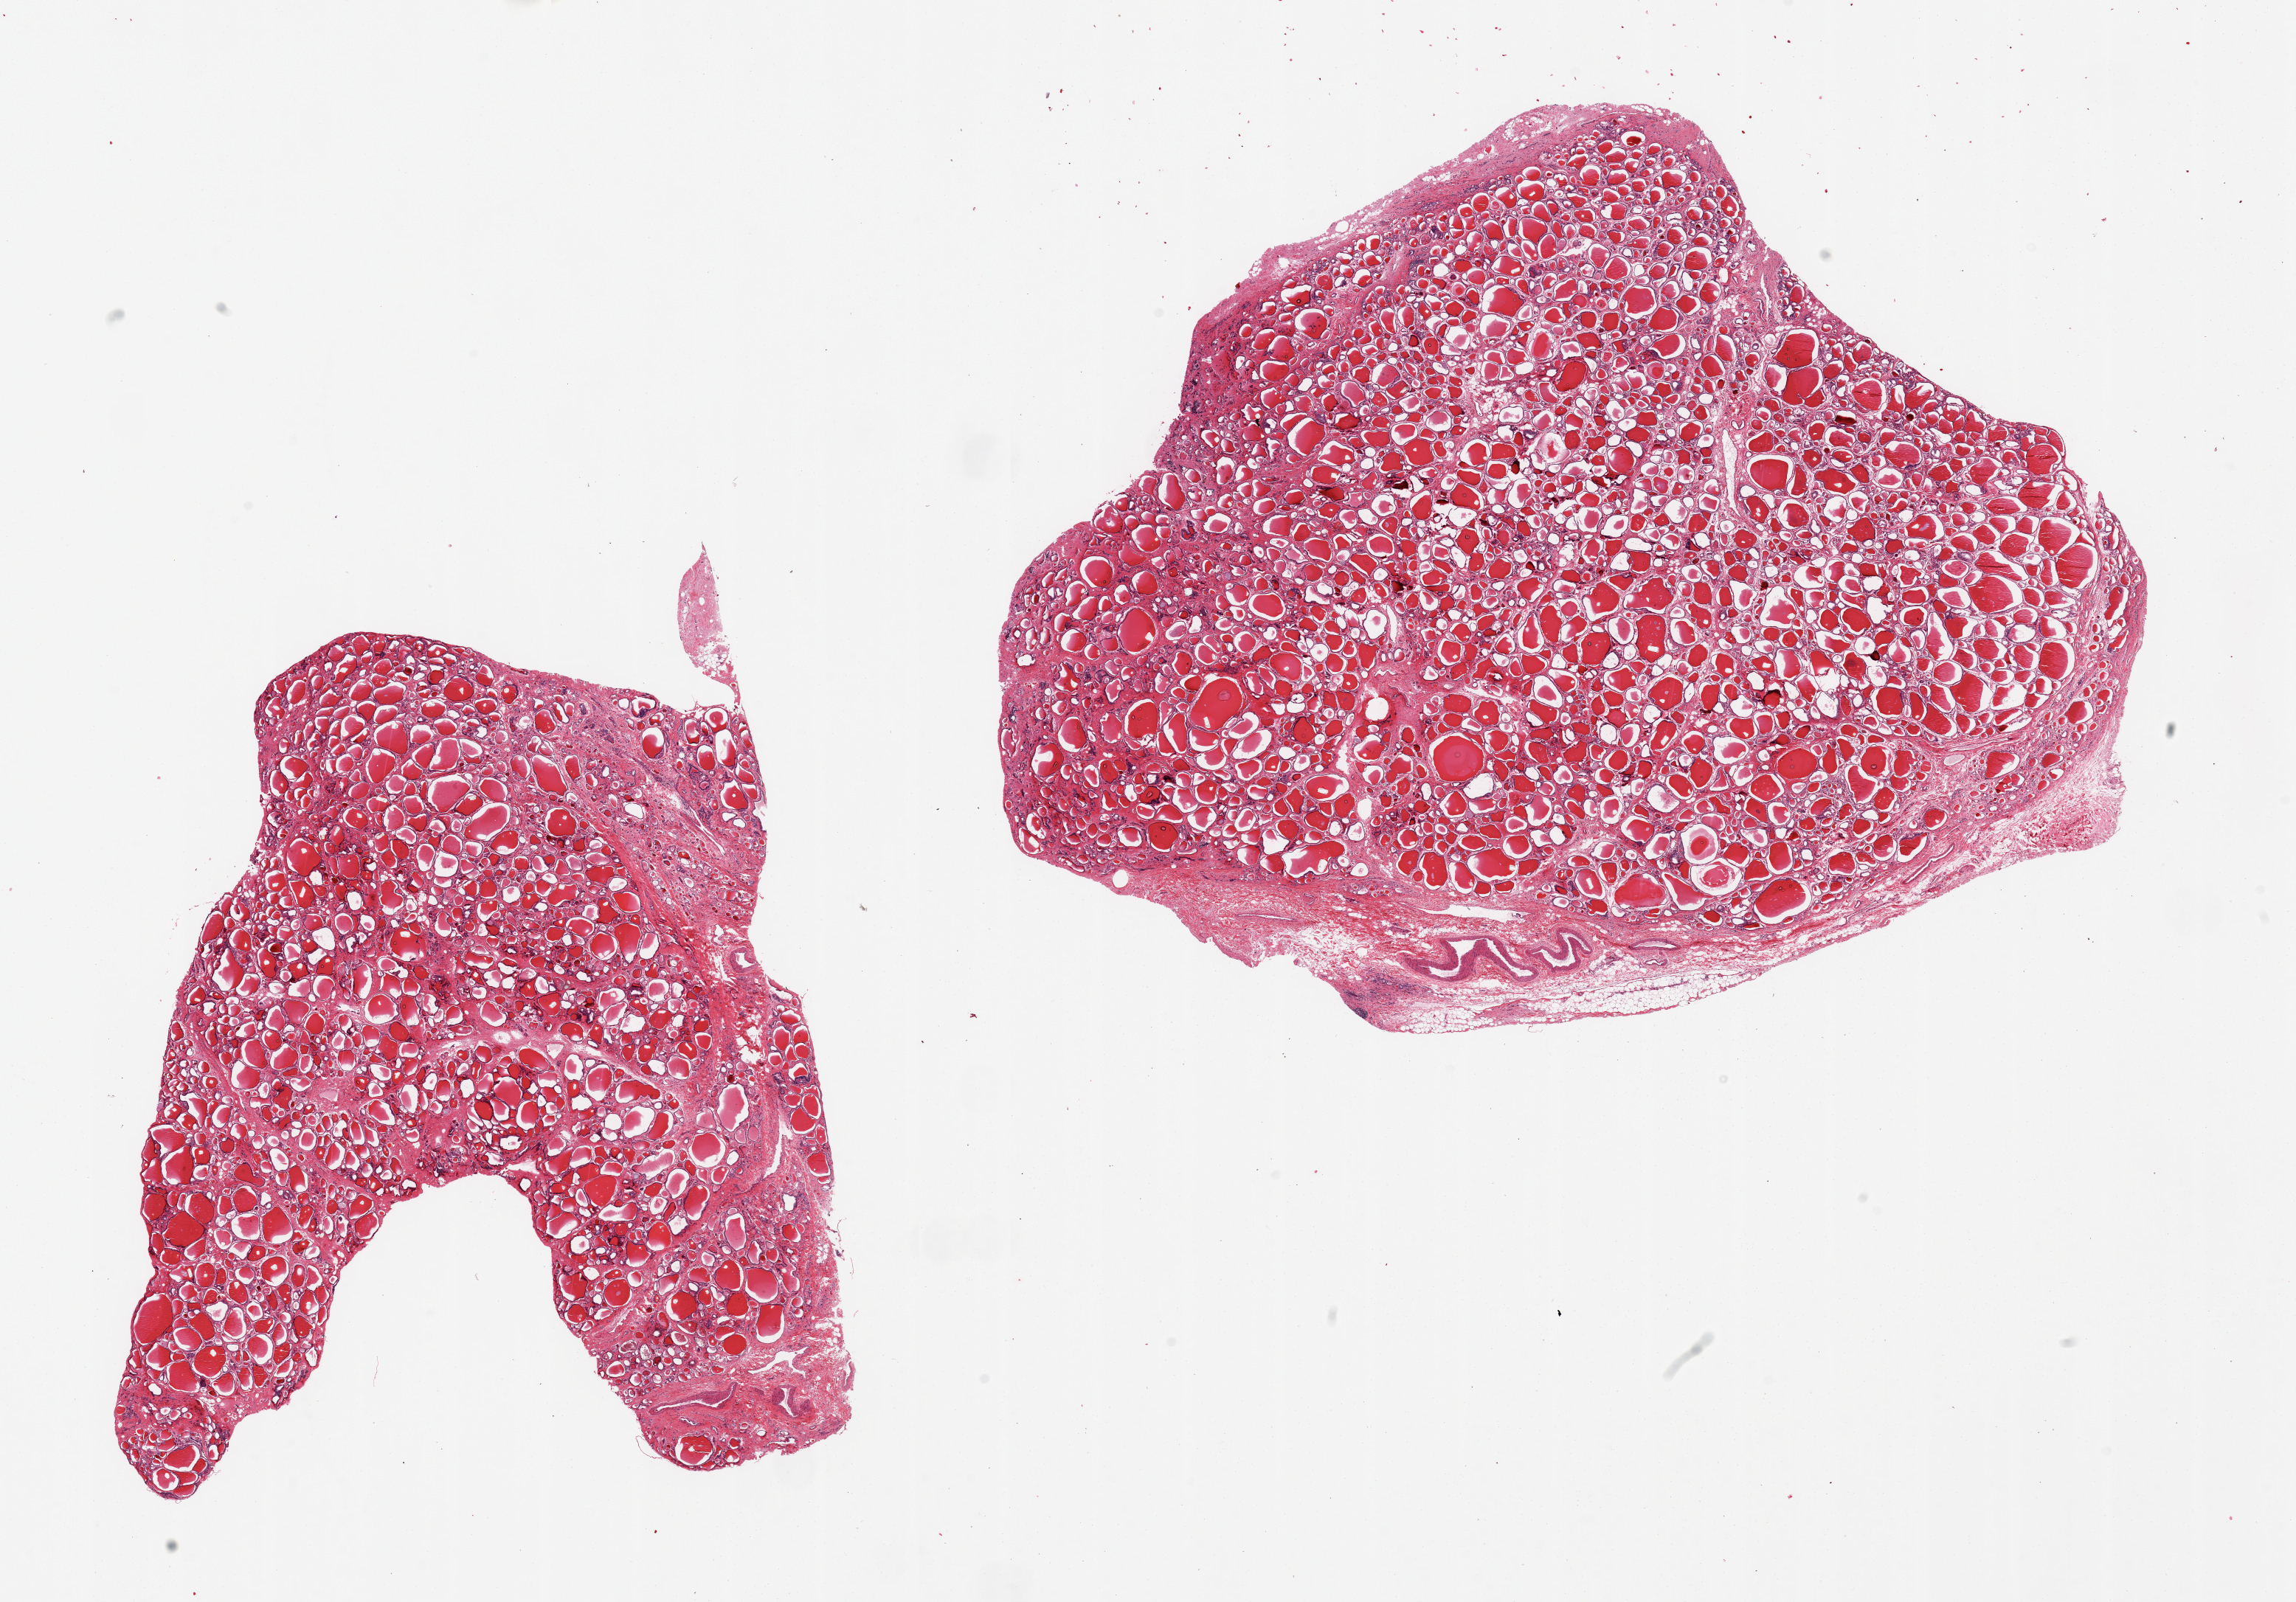
Whole-slide image, haematoxylin and eosin stain, whole scanned area (about 24.6 x 17.2 mm) shown as a low-resolution overview, PAXgene-fixed, paraffin-embedded tissue, sampled site (target tissue): thyroid, tissue donor sample.
Reviewer comment on this tissue sample: 2 pieces; multifocal mild stromal fibrosis compromising thyroid follicles.